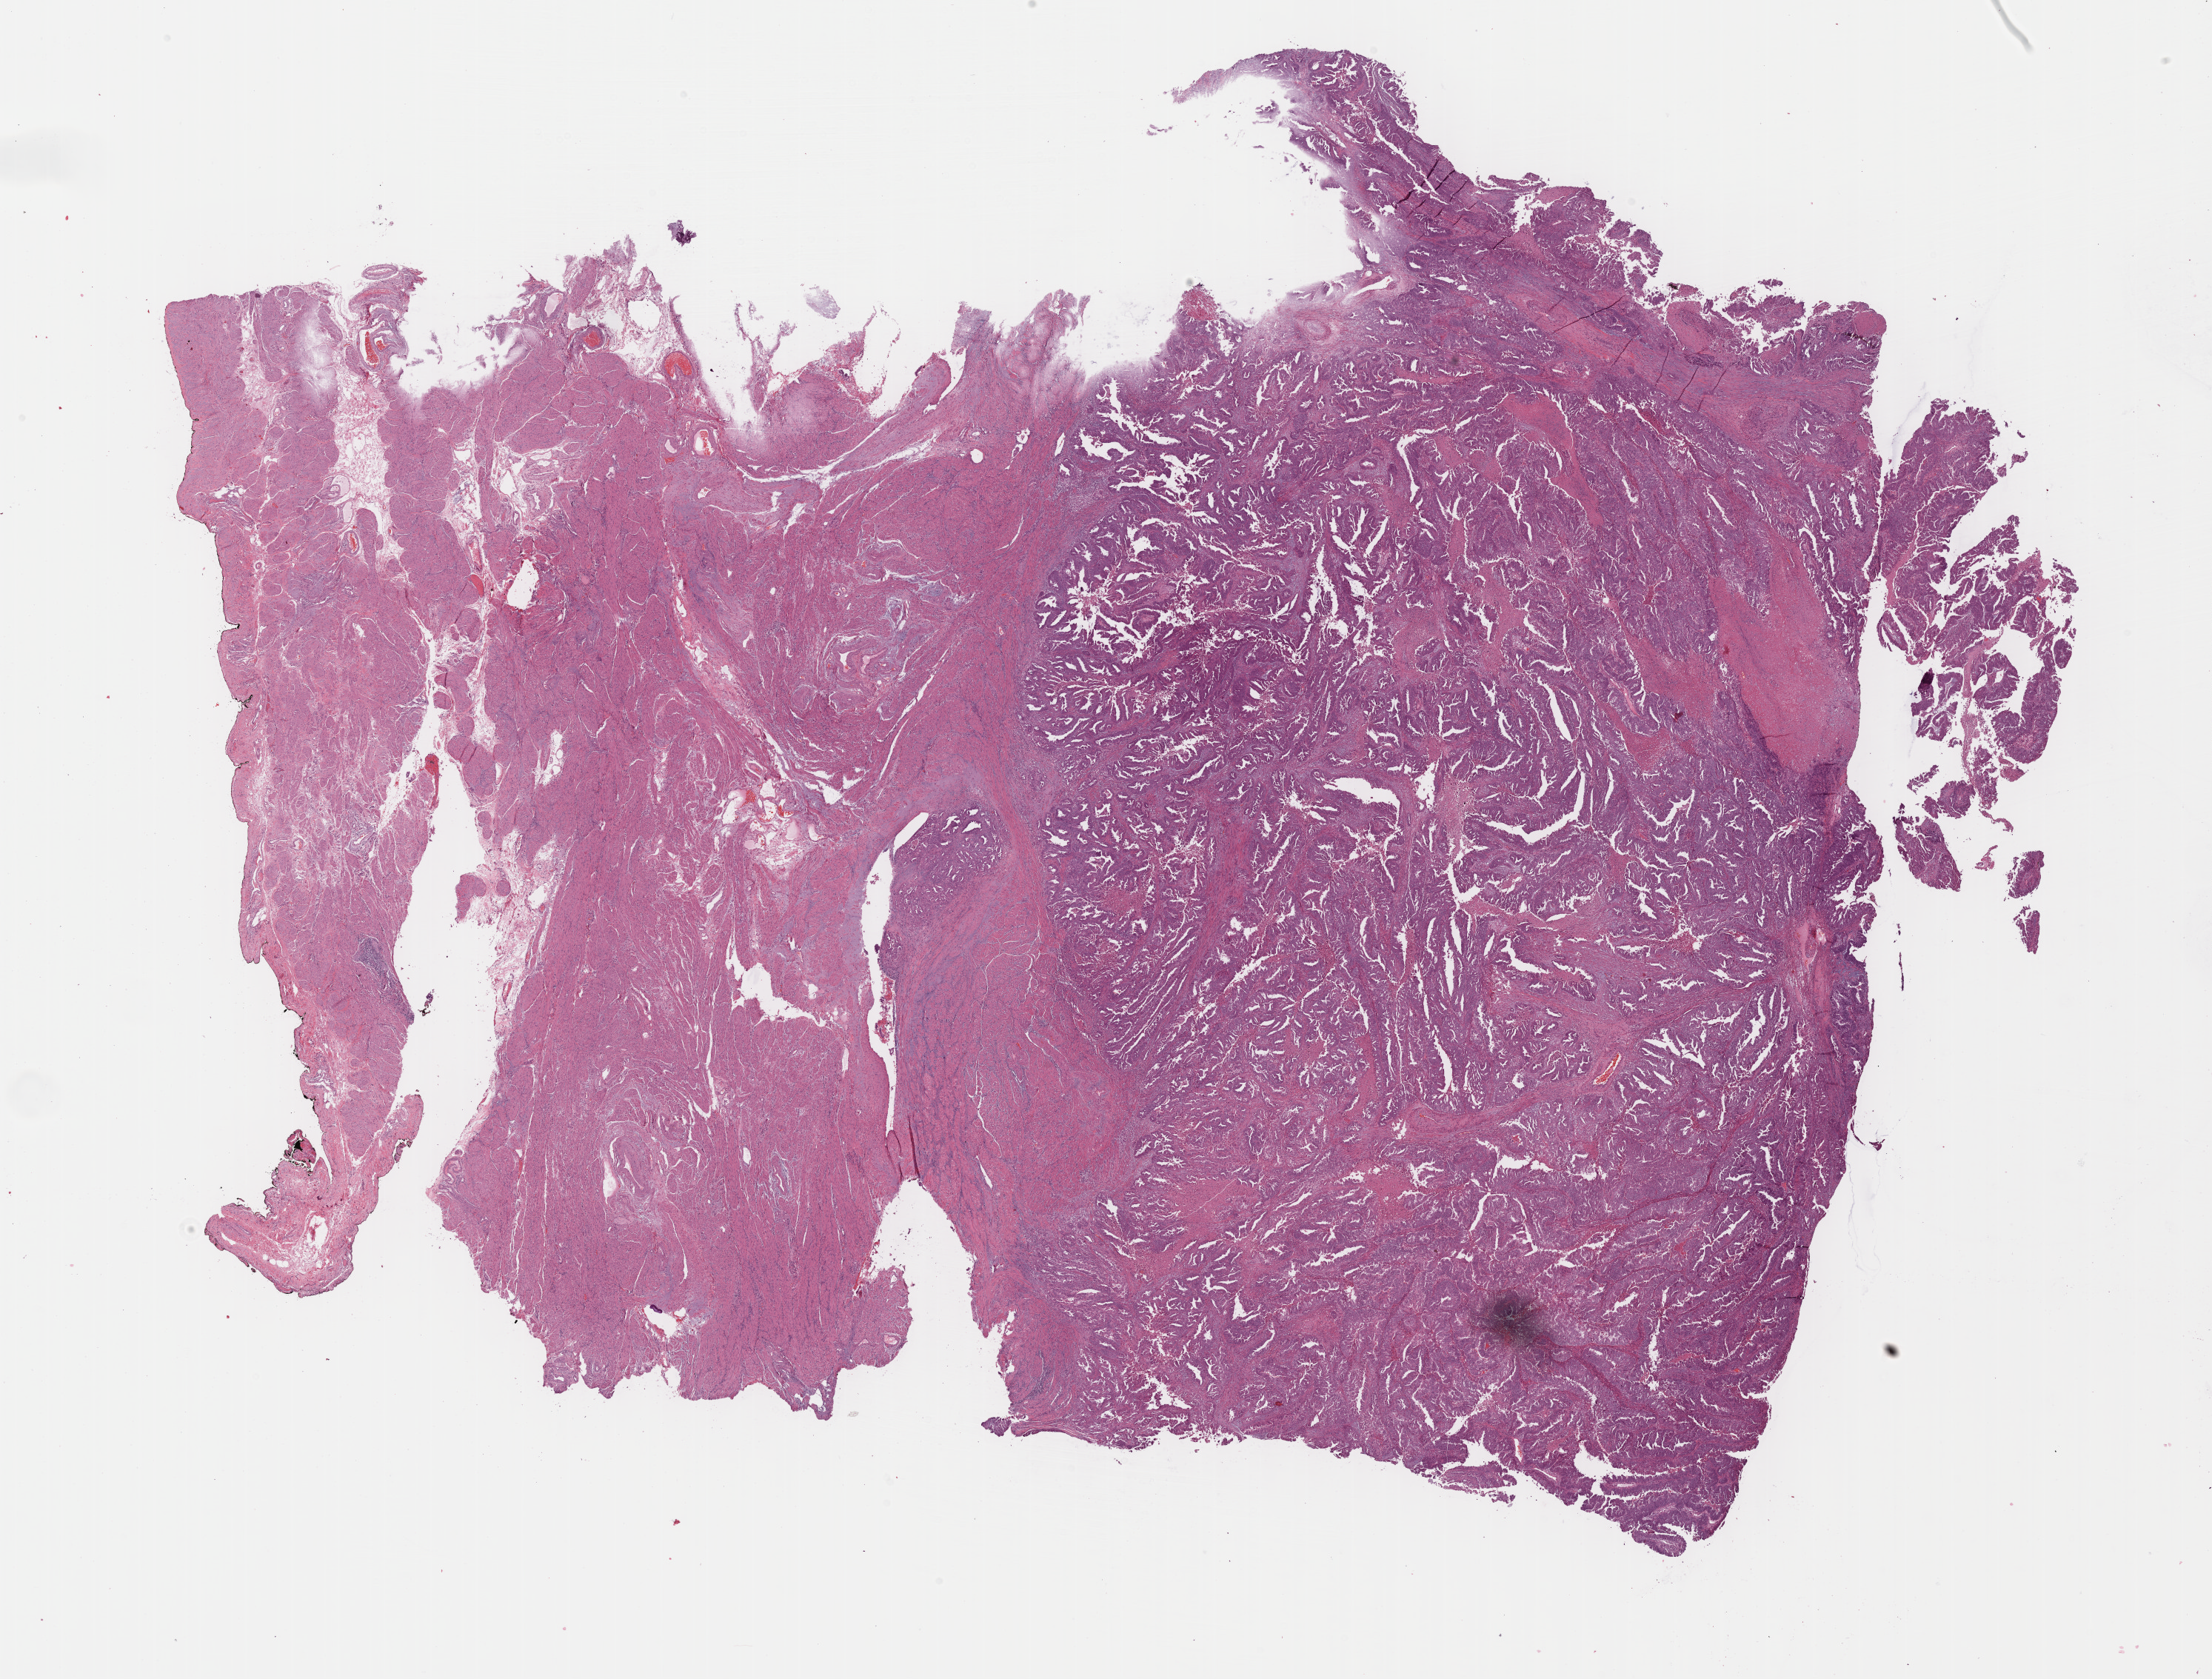
Digitized H&E tissue section (whole slide) — shown as a low-resolution overview of the whole scanned area (about 24.2 x 18.3 mm). Formalin-fixed paraffin-embedded (FFPE) diagnostic section. Uterus, primary tumour sample. Female, age 77 years at initial diagnosis. Histologic grade: G3 (poorly differentiated).
* FIGO stage: IB
* histologic diagnosis: Endometrioid adenocarcinoma, NOS (endometrium)